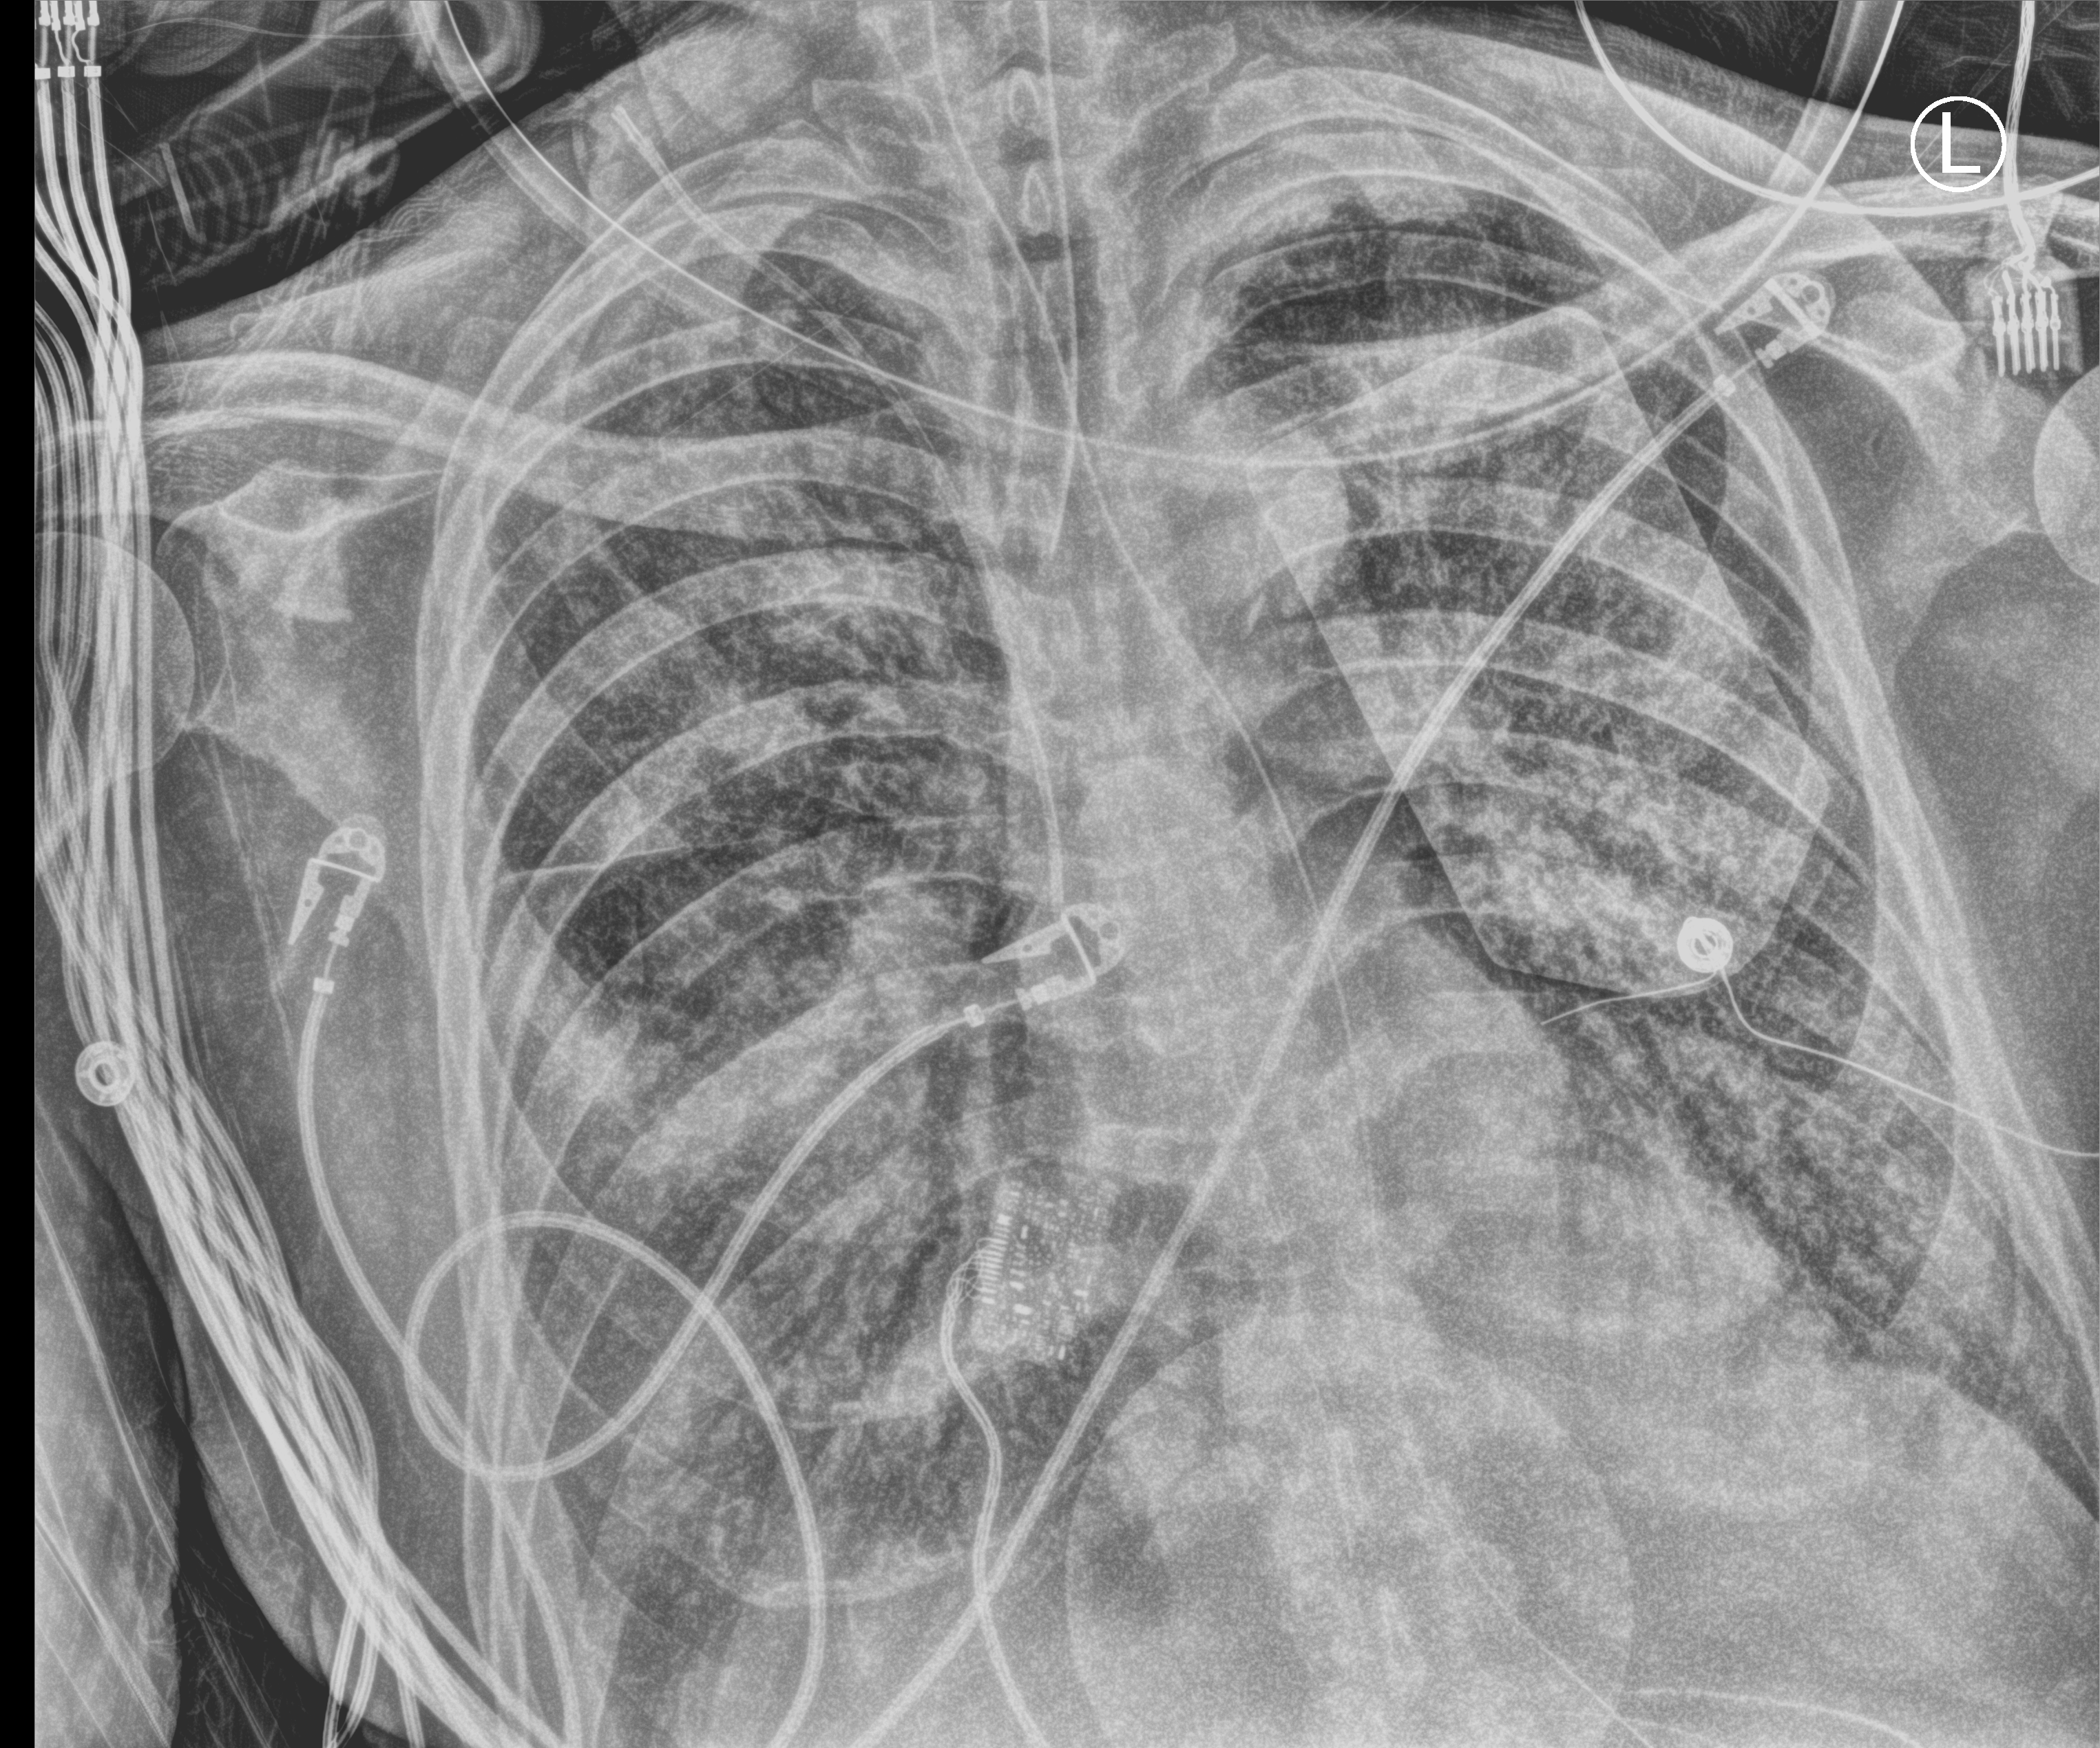
Portable chest radiograph; anteroposterior (AP) projection. Male patient hospitalised with COVID-19, age 60–74 years.
Admission-level facts for this patient (not findings on this image; timing relative to this image not recorded): length of hospital stay: 31 days; mechanically ventilated during this hospital stay: yes.